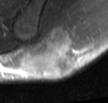
MRI of an extremity soft-tissue mass, one axial slice; position 17 of 42 along the scan axis; T2-weighted fat-saturated; MR volume resampled by the dataset authors to the PET/CT grid (not the native acquisition matrix); 3.27 mm slice thickness; 108 × 103 image matrix. Male patient. Case-level facts recorded for this patient, not image findings: histological type: leiomyosarcoma; grade: intermediate; site of the primary tumour: left pelvis.
Structures marked on this image (expert contour drawn on MRI and transferred to this co-registered scan by the dataset authors):
- gross tumour volume (mass): bounding box <25,26,77,77> (left, top, right, bottom; pixels)